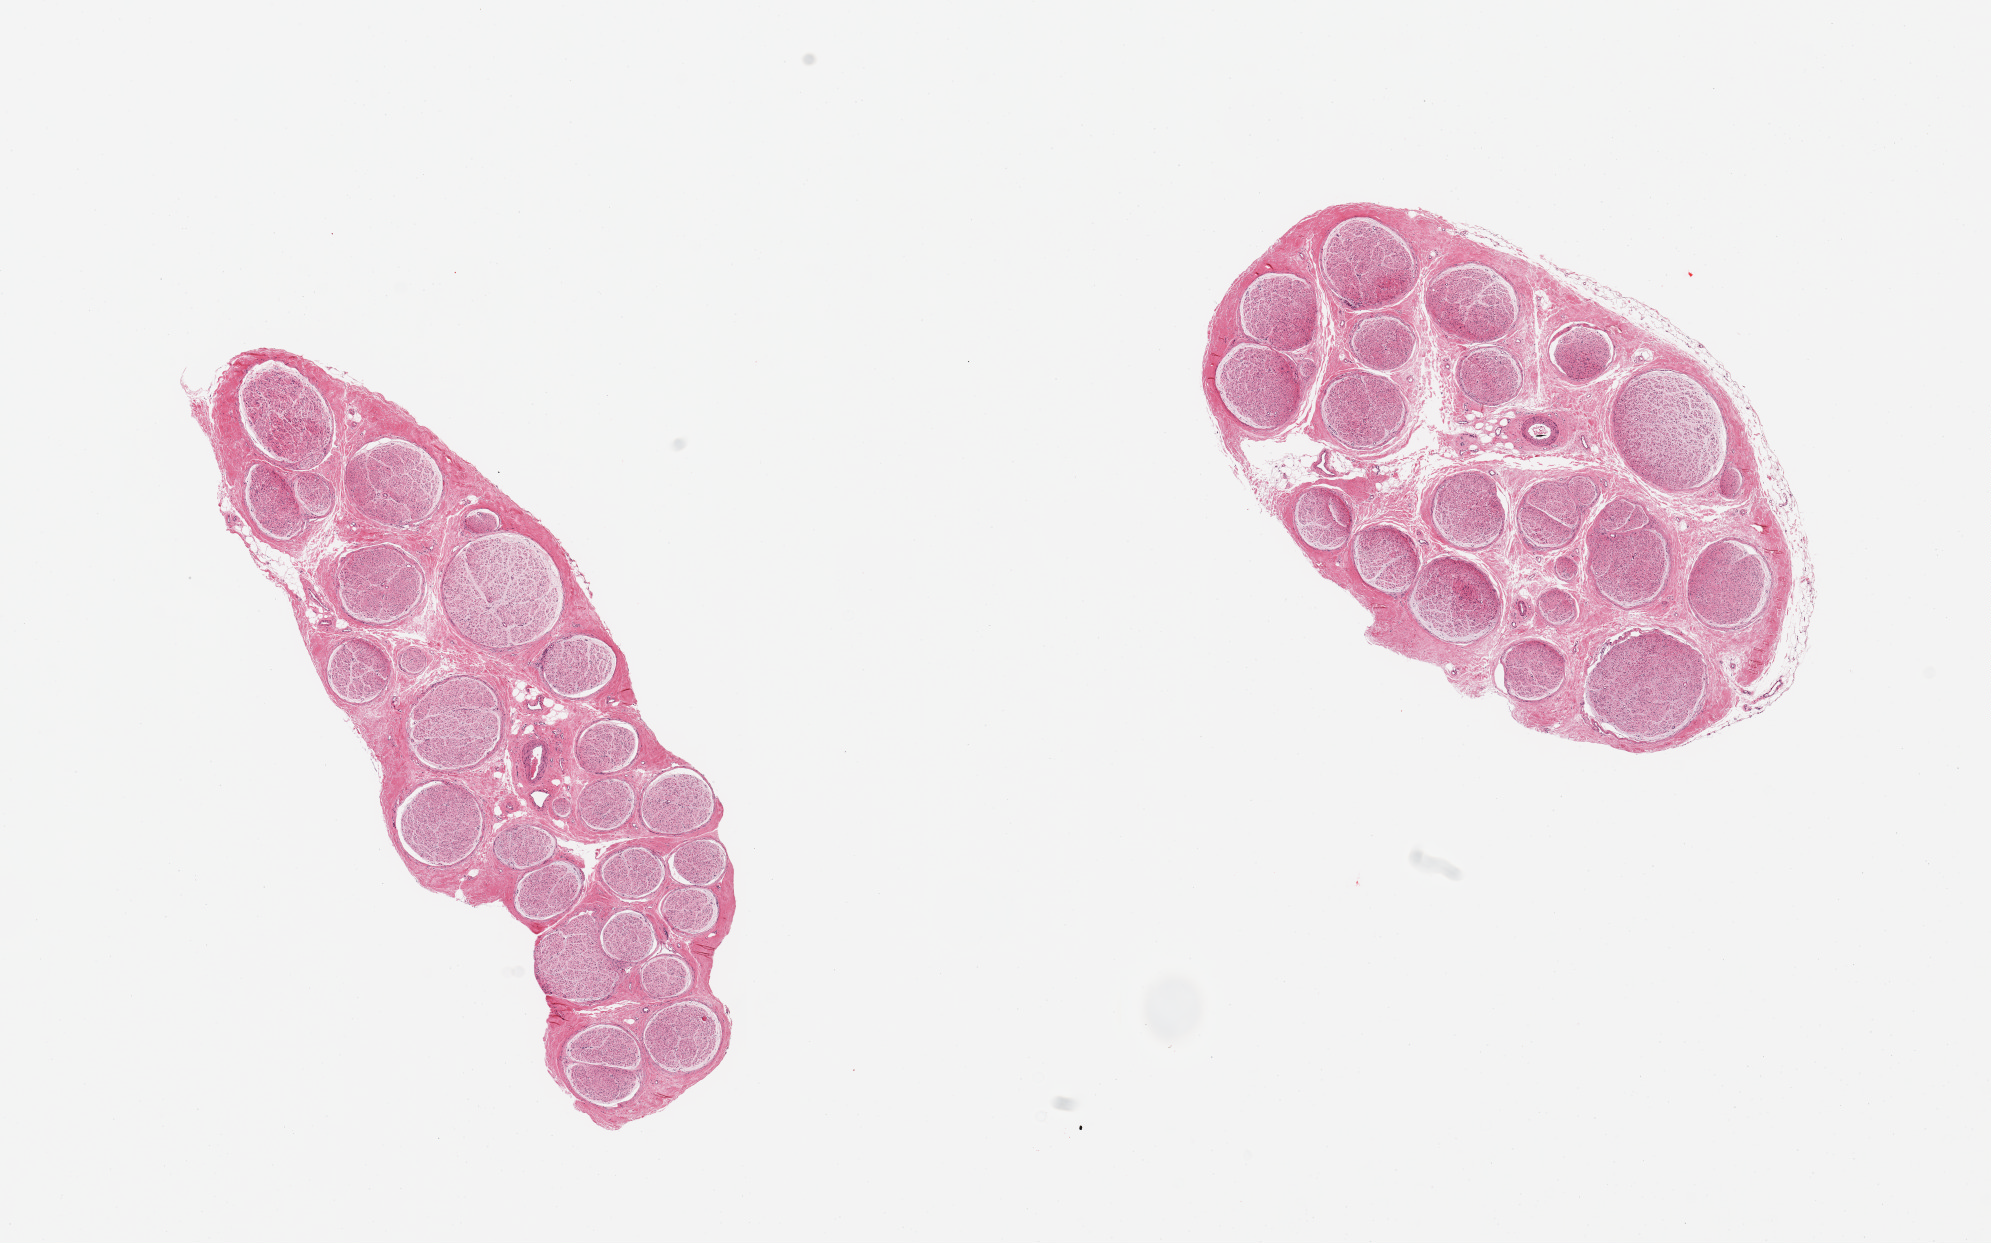
Whole-slide image, hematoxylin and eosin (H&E) stain, brightfield, whole scanned area (about 15.8 x 9.8 mm) shown as a low-resolution overview, PAXgene-fixed paraffin-embedded (PFPE) section, sampled site (target tissue): tibial nerve, tissue donor sample. Male donor.
Pathologist's review note for this sample: 2 pieces, minimal adherent fat.